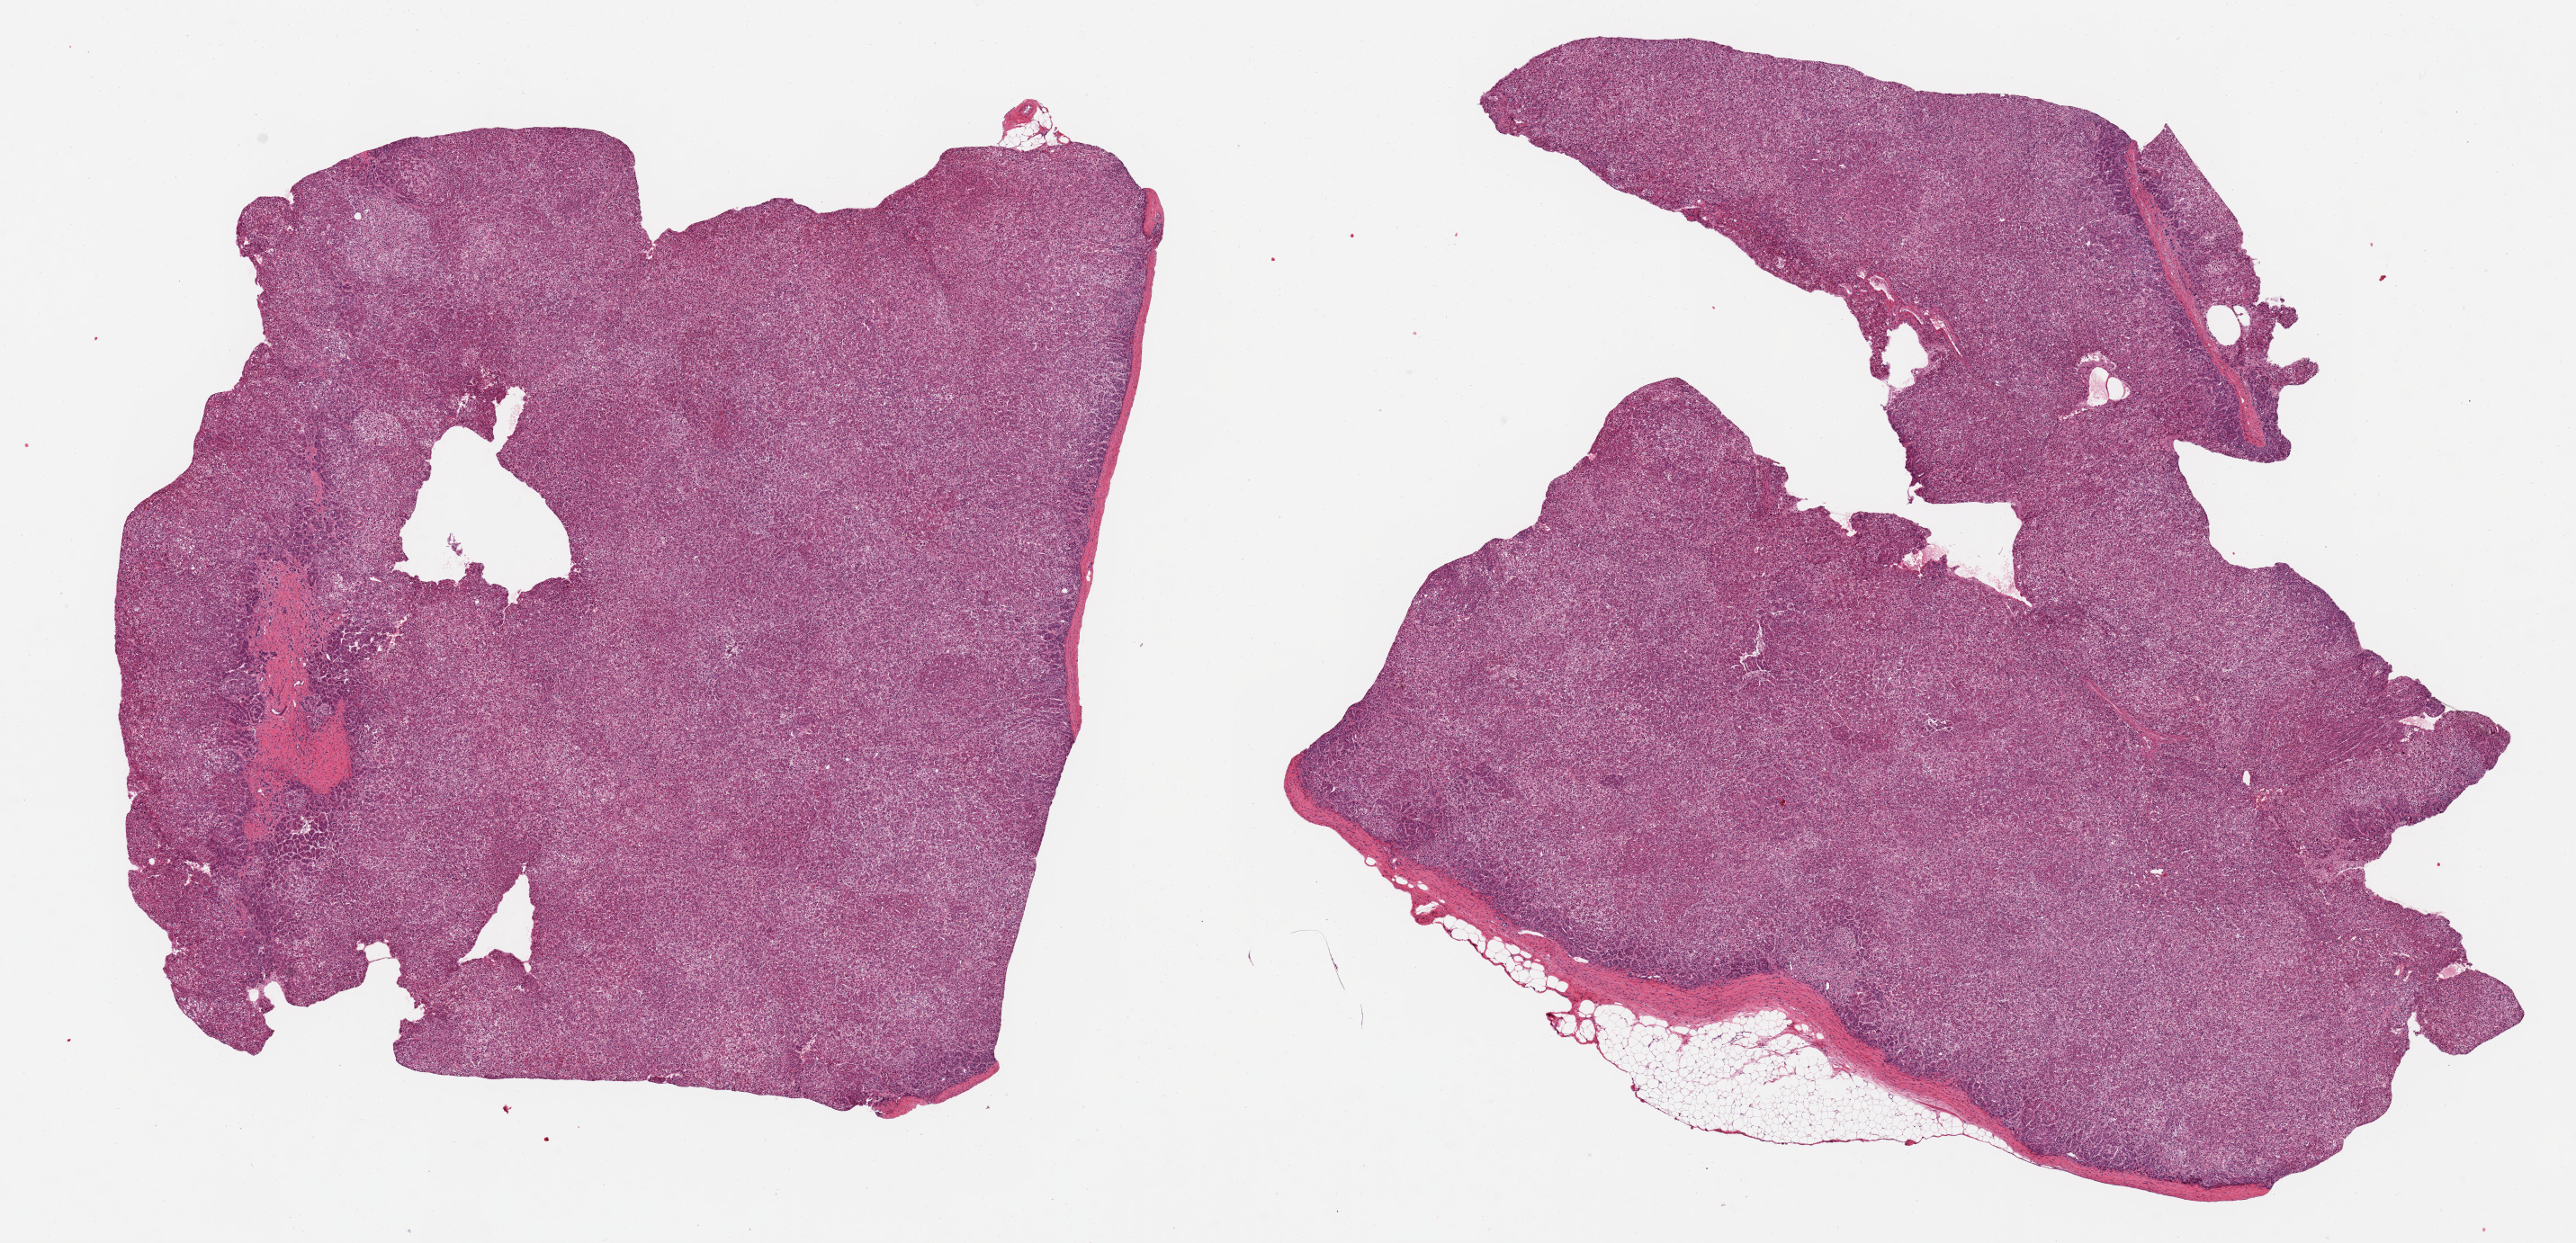
Digitized hematoxylin and eosin (H&E)-stained section, low-resolution overview of the scanned area, about 22.6 x 10.9 mm, PAXgene-fixed paraffin-embedded (PFPE) section, sampled site (target tissue): adrenal gland, donor tissue sample. Donor: male.
Pathologist's review note for this sample: 2 aliquots, ~10x7mm. All cortex. Unusually well-preserved.